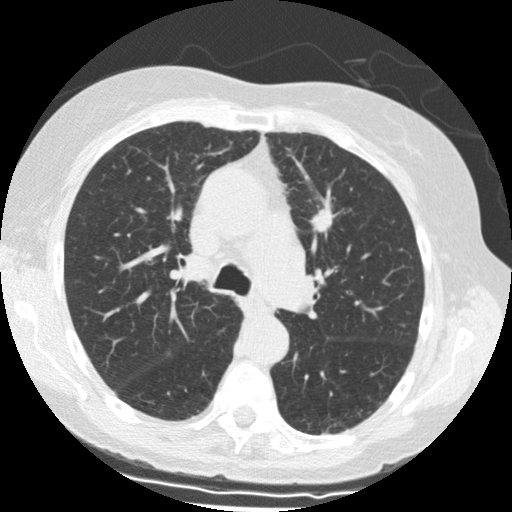
Chest CT (low-dose screening protocol), one axial image; baseline screening round; lung window (W 1500 / L -600 HU); standard (soft-tissue) reconstruction kernel (STANDARD). Female, age 69 years at enrolment. Former smoker at enrolment.
Lesion marked by an expert reader, bounding box <299,206,345,247> (left, top, right, bottom; pixels). The screening reader recorded 2 non-calcified nodules or masses ≥4 mm on this exam (left upper lobe, left upper lobe); which of them this box marks is not recorded. Lung cancer was diagnosed 18 days after this screen: squamous cell carcinoma, NOS, left upper lobe, stage IIIA (AJCC 6th edition), 15 mm at pathology.